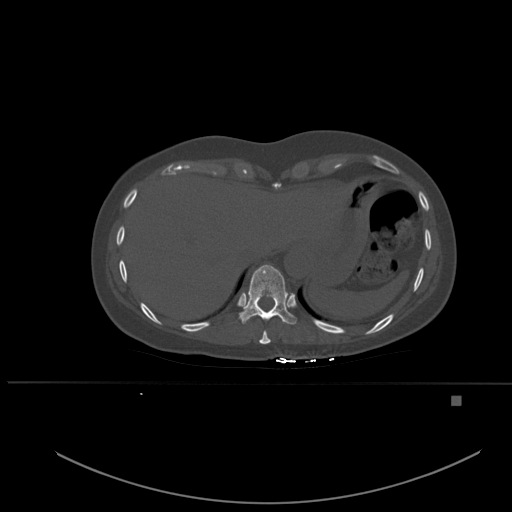
CT including the spine, one axial slice; position 292 of 651 along the scan axis; bone window (W 1800 / L 400 HU); 512 × 512 image matrix. Patient: female, 49 years. From the clinical record (not read from this slice): primary cancer: breast; vertebrae with lytic lesions (as recorded): L3, T12, L4.
Structures marked on this image (semi-automatic segmentation, software-assisted and operator-edited):
- T10 vertebra: box from (x=239, y=265) to (x=297, y=325) px
- T9 vertebra: (x=259, y=330)–(x=271, y=344)